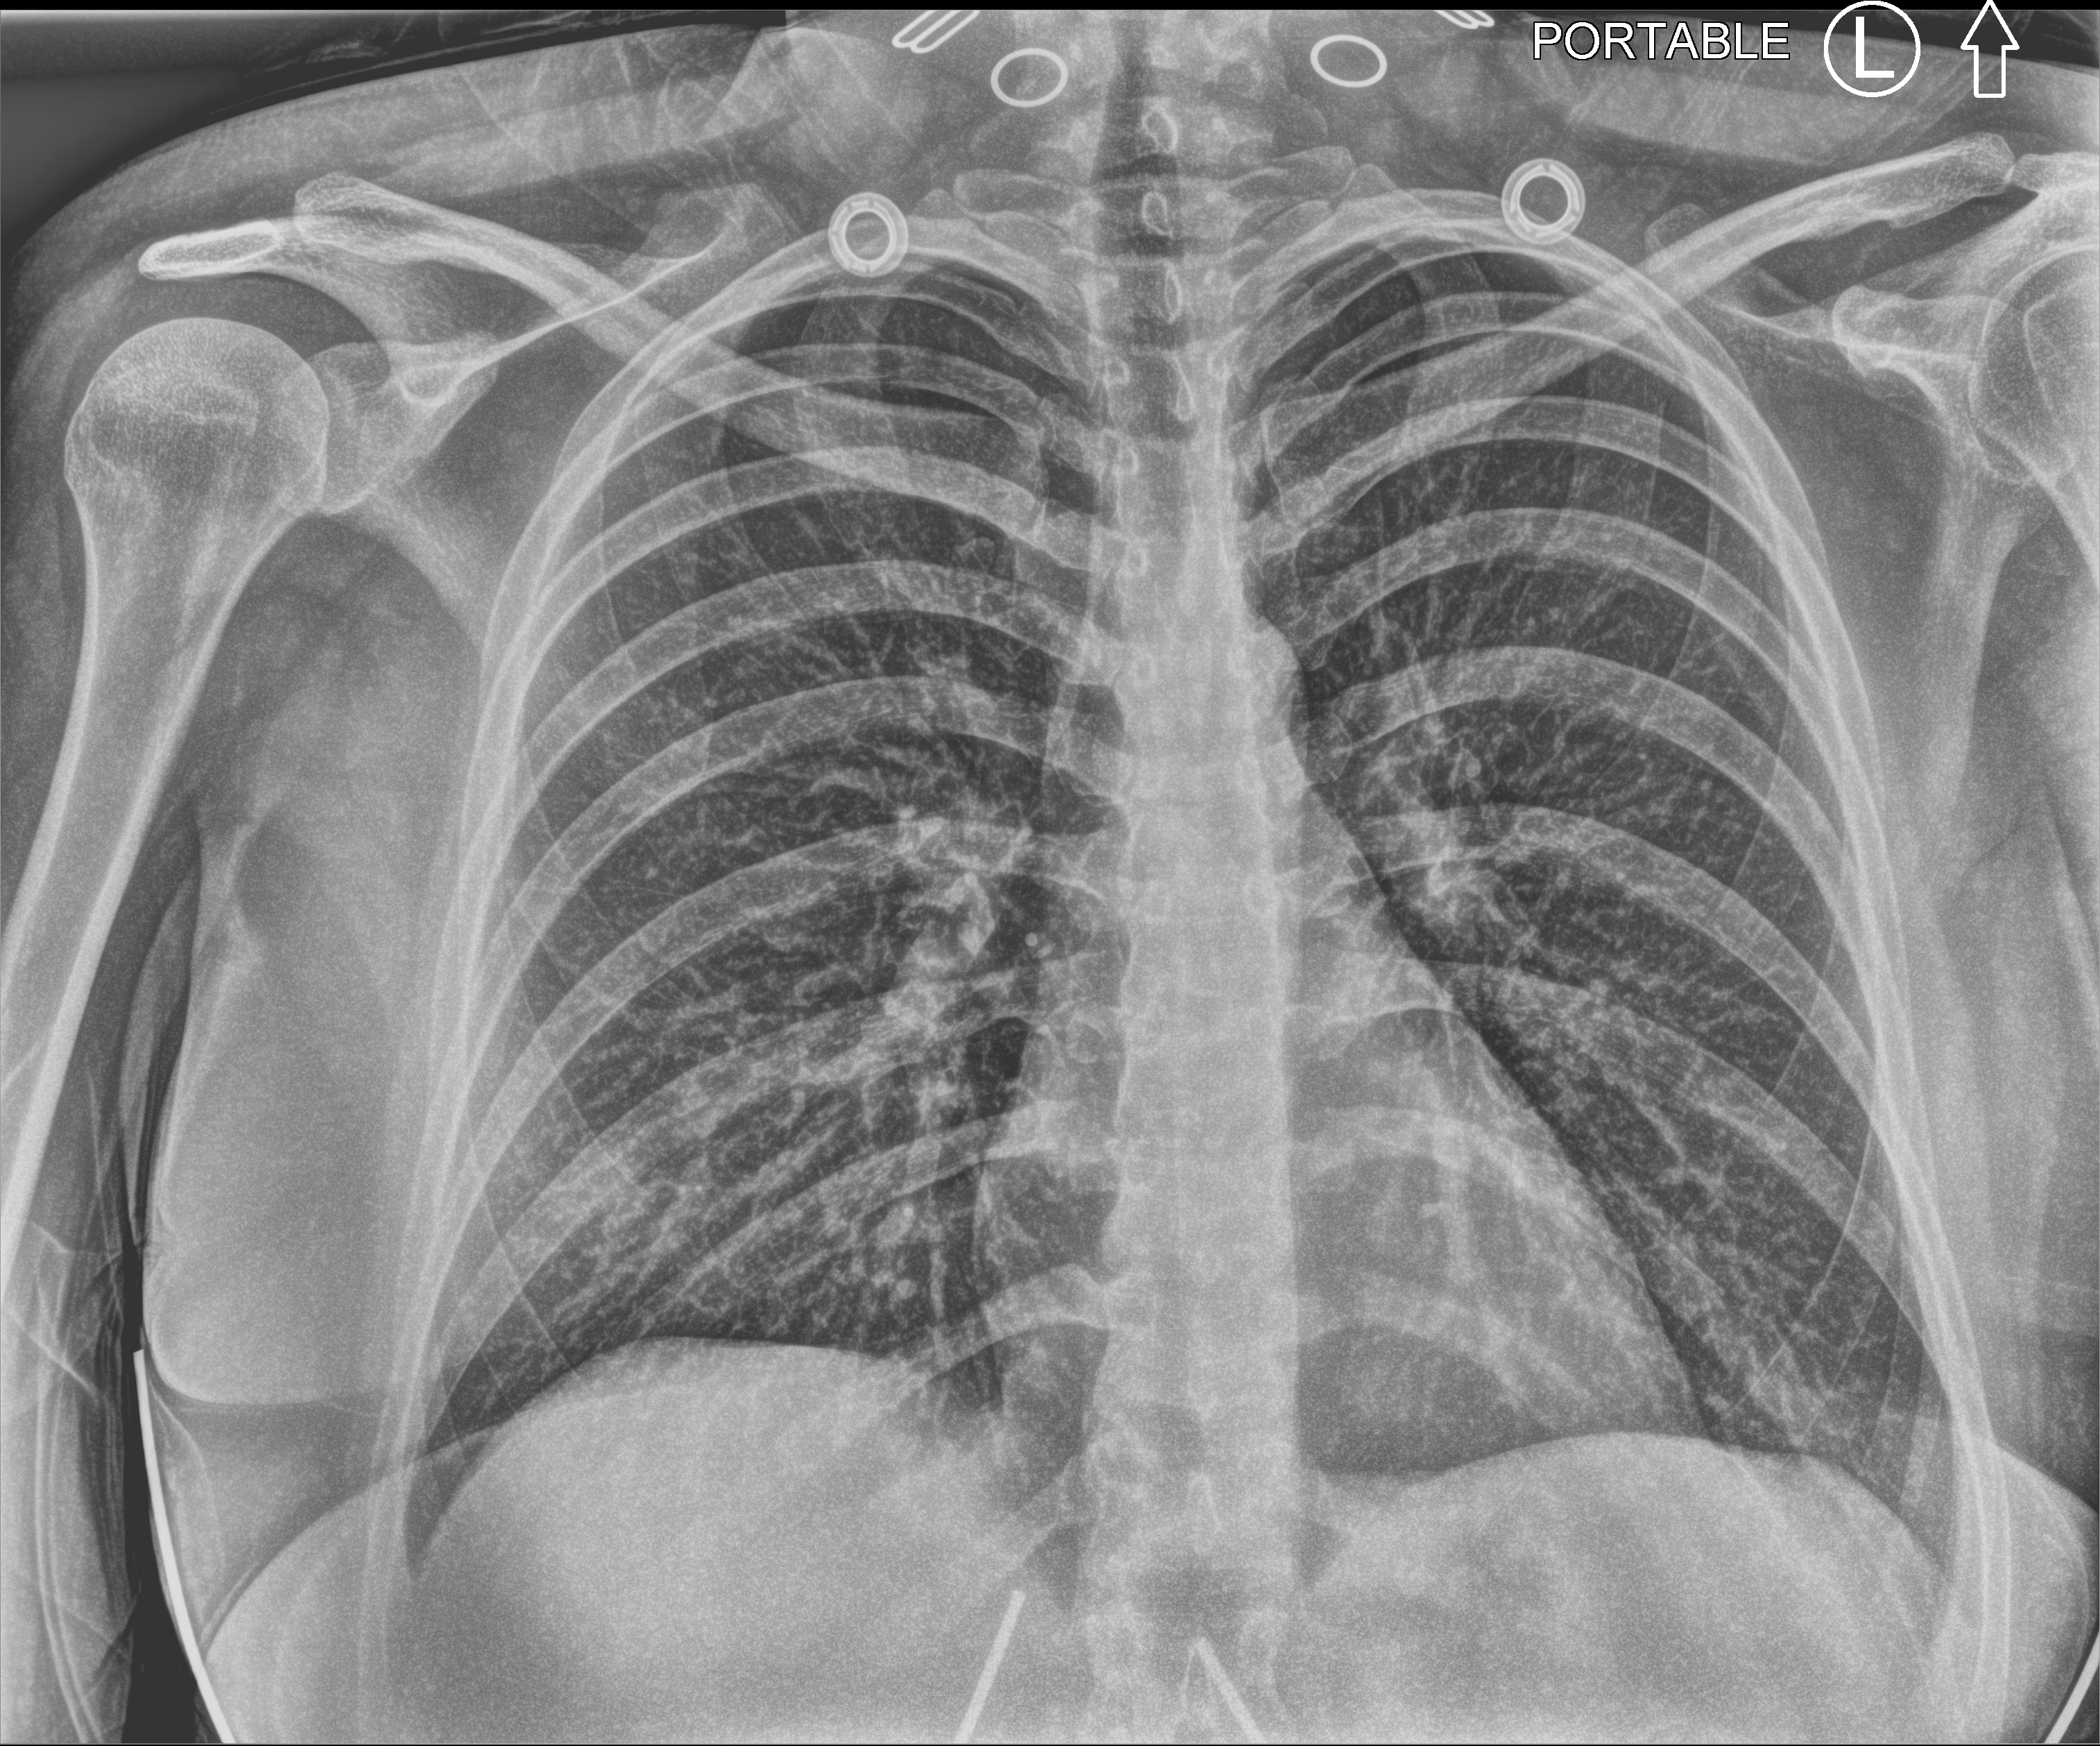
Chest X-ray (portable), anteroposterior (AP) projection. Female patient hospitalised with COVID-19, age 18–59 years.
From the hospital-stay record, not from the radiograph (when in the stay this image was taken is not recorded):
- admitted to intensive care during this hospital stay: no
- mechanically ventilated during this hospital stay: no